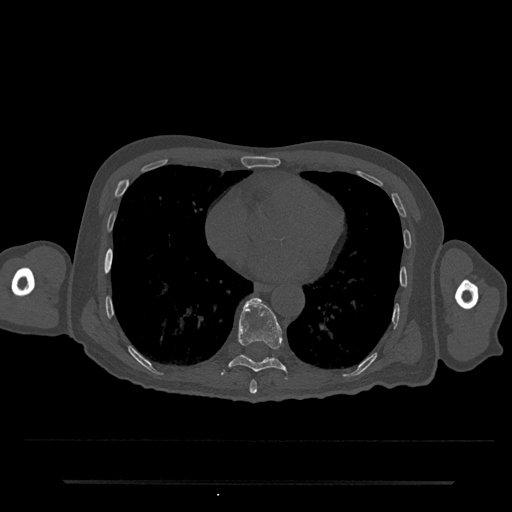
CT including the spine, one axial slice. Slice 365 of 797 in the series (ordered by position). Reconstruction kernel Br40s/3. 120 kVp. Bone window (W 1800 / L 400 HU). 0.5 mm slice thickness. 512 × 512 image matrix. Male patient, age 74 years. From the clinical record (not read from this slice): primary cancer: prostate.
Outlined on this slice (semi-automatic segmentation, software-assisted and operator-edited):
- T8 vertebra: bounding box (x1, y1, x2, y2) in pixels: (249, 380, 257, 394)
- T9 vertebra: (222, 298, 288, 378)